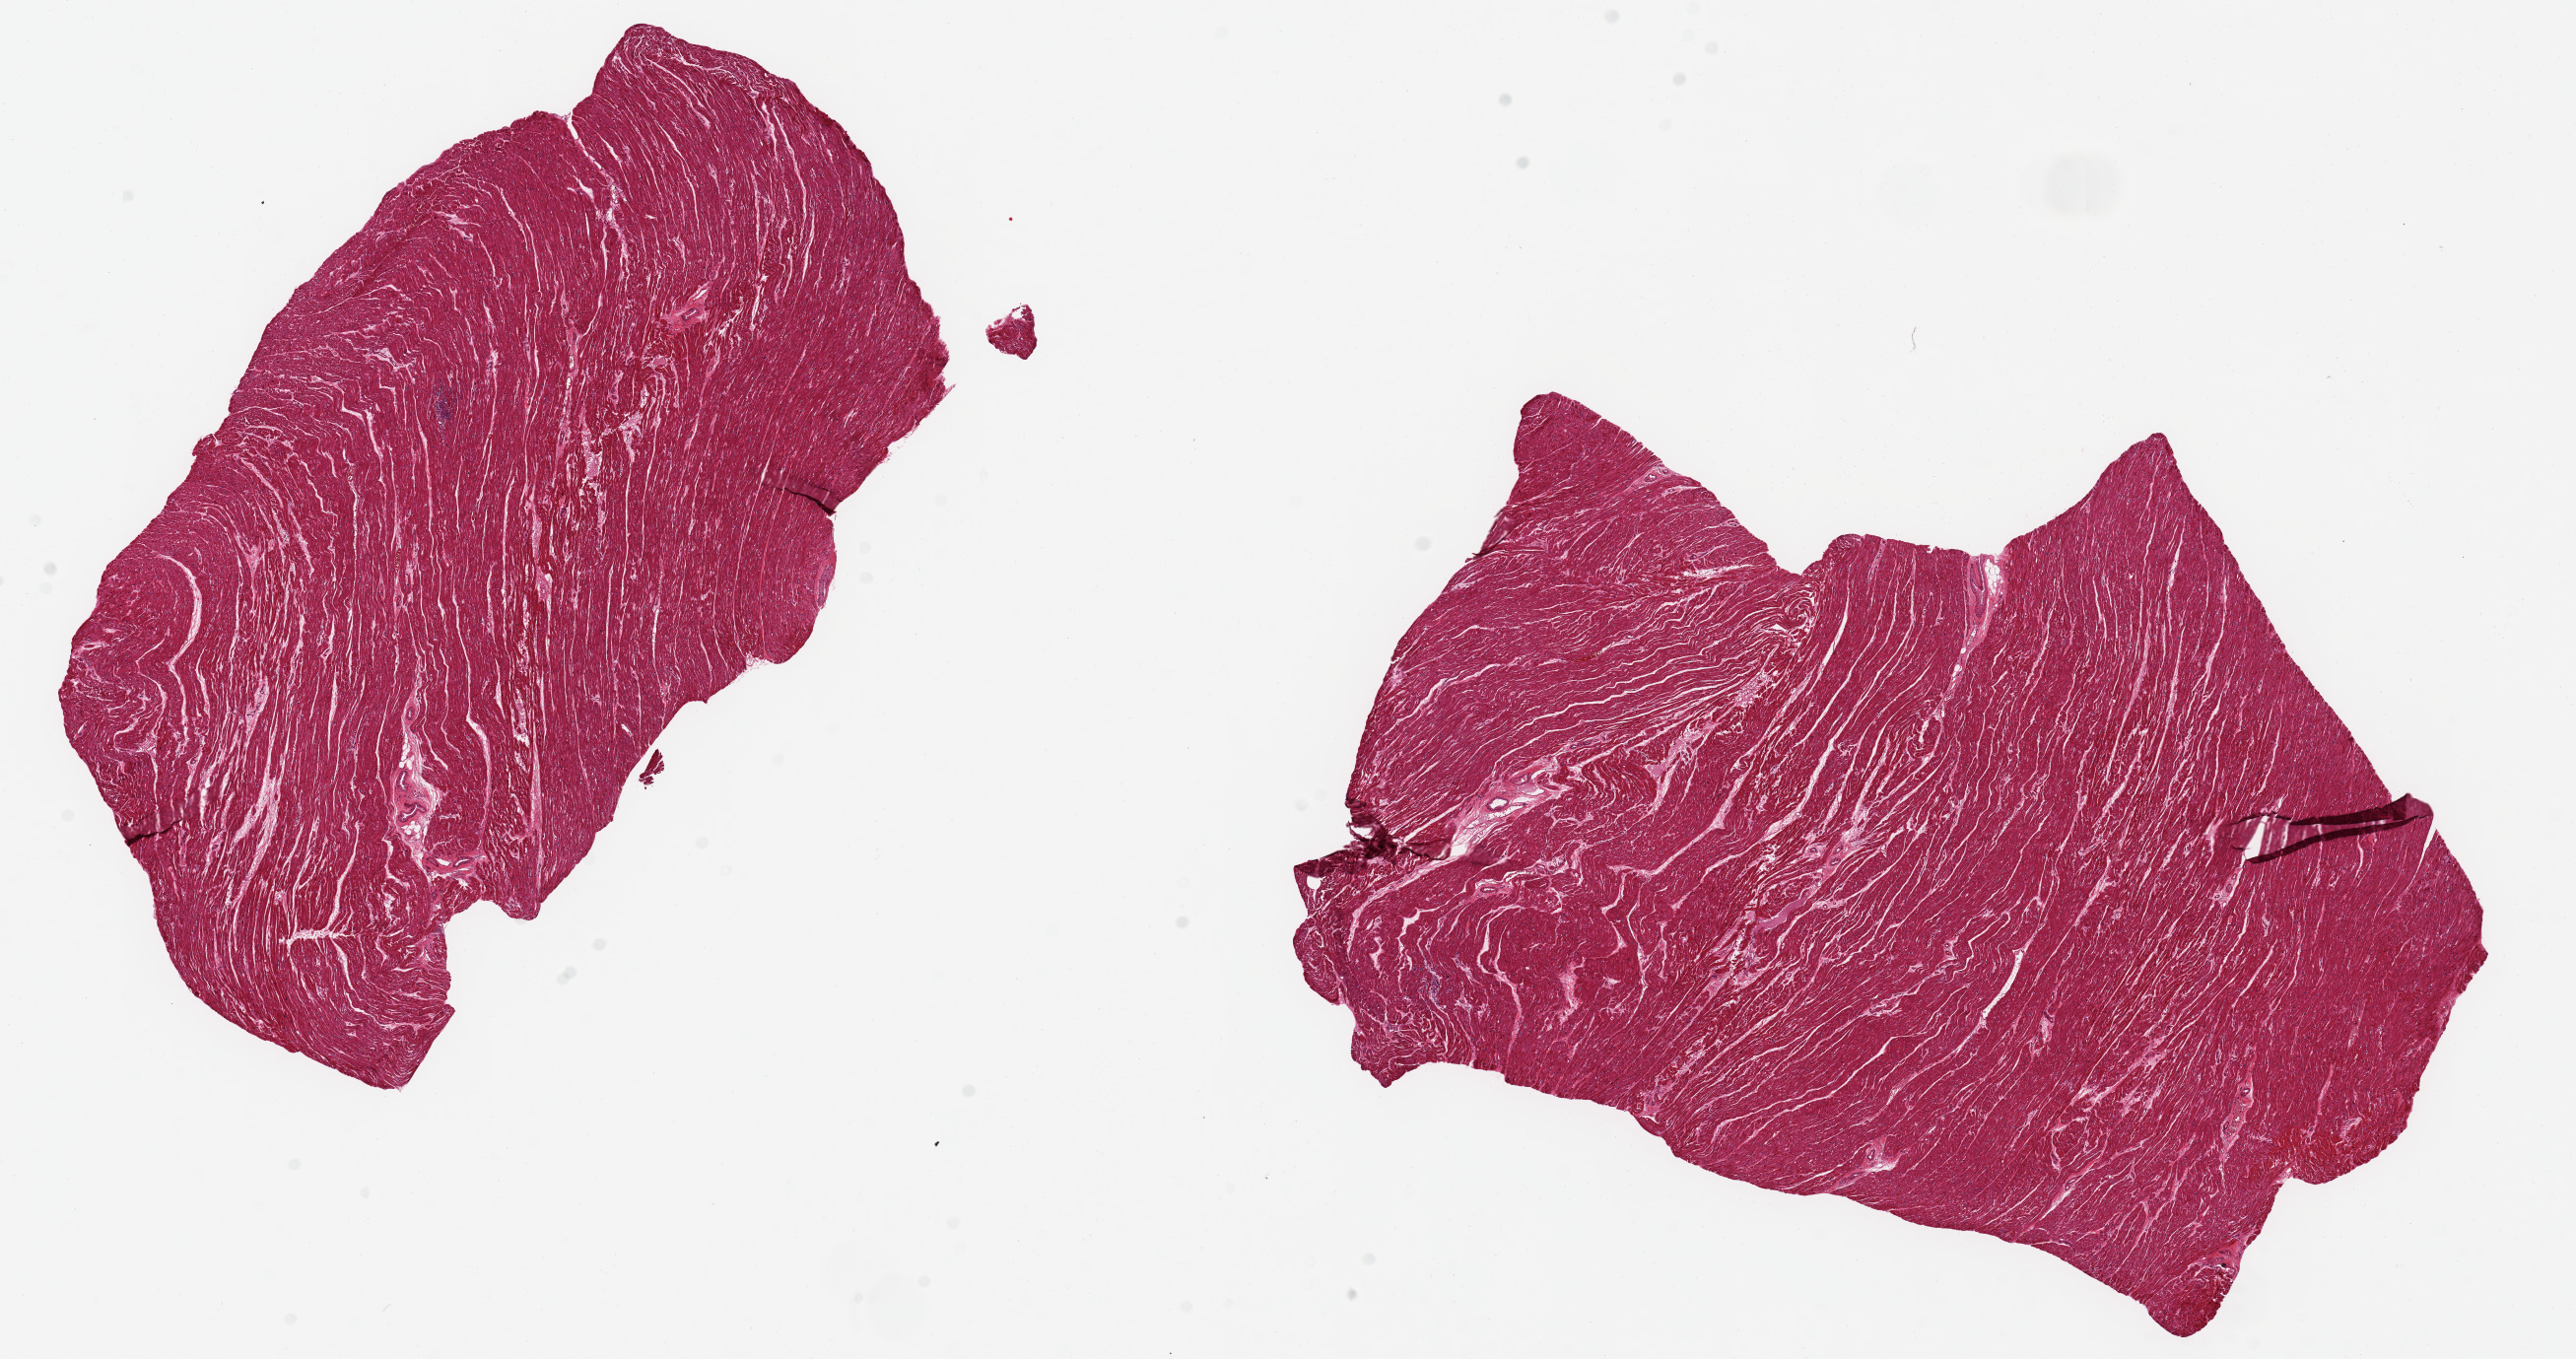
Haematoxylin and eosin whole-slide image — a low-resolution overview of the entire scanned area, about 20.7 x 10.9 mm; PAXgene-fixed, paraffin-embedded tissue; sampled site (target tissue): heart; donor tissue sample. Donor sex: male.
Review note (as recorded): 2 pieces, 9x5 & 9x7mm; muscle without extraneous adipose.